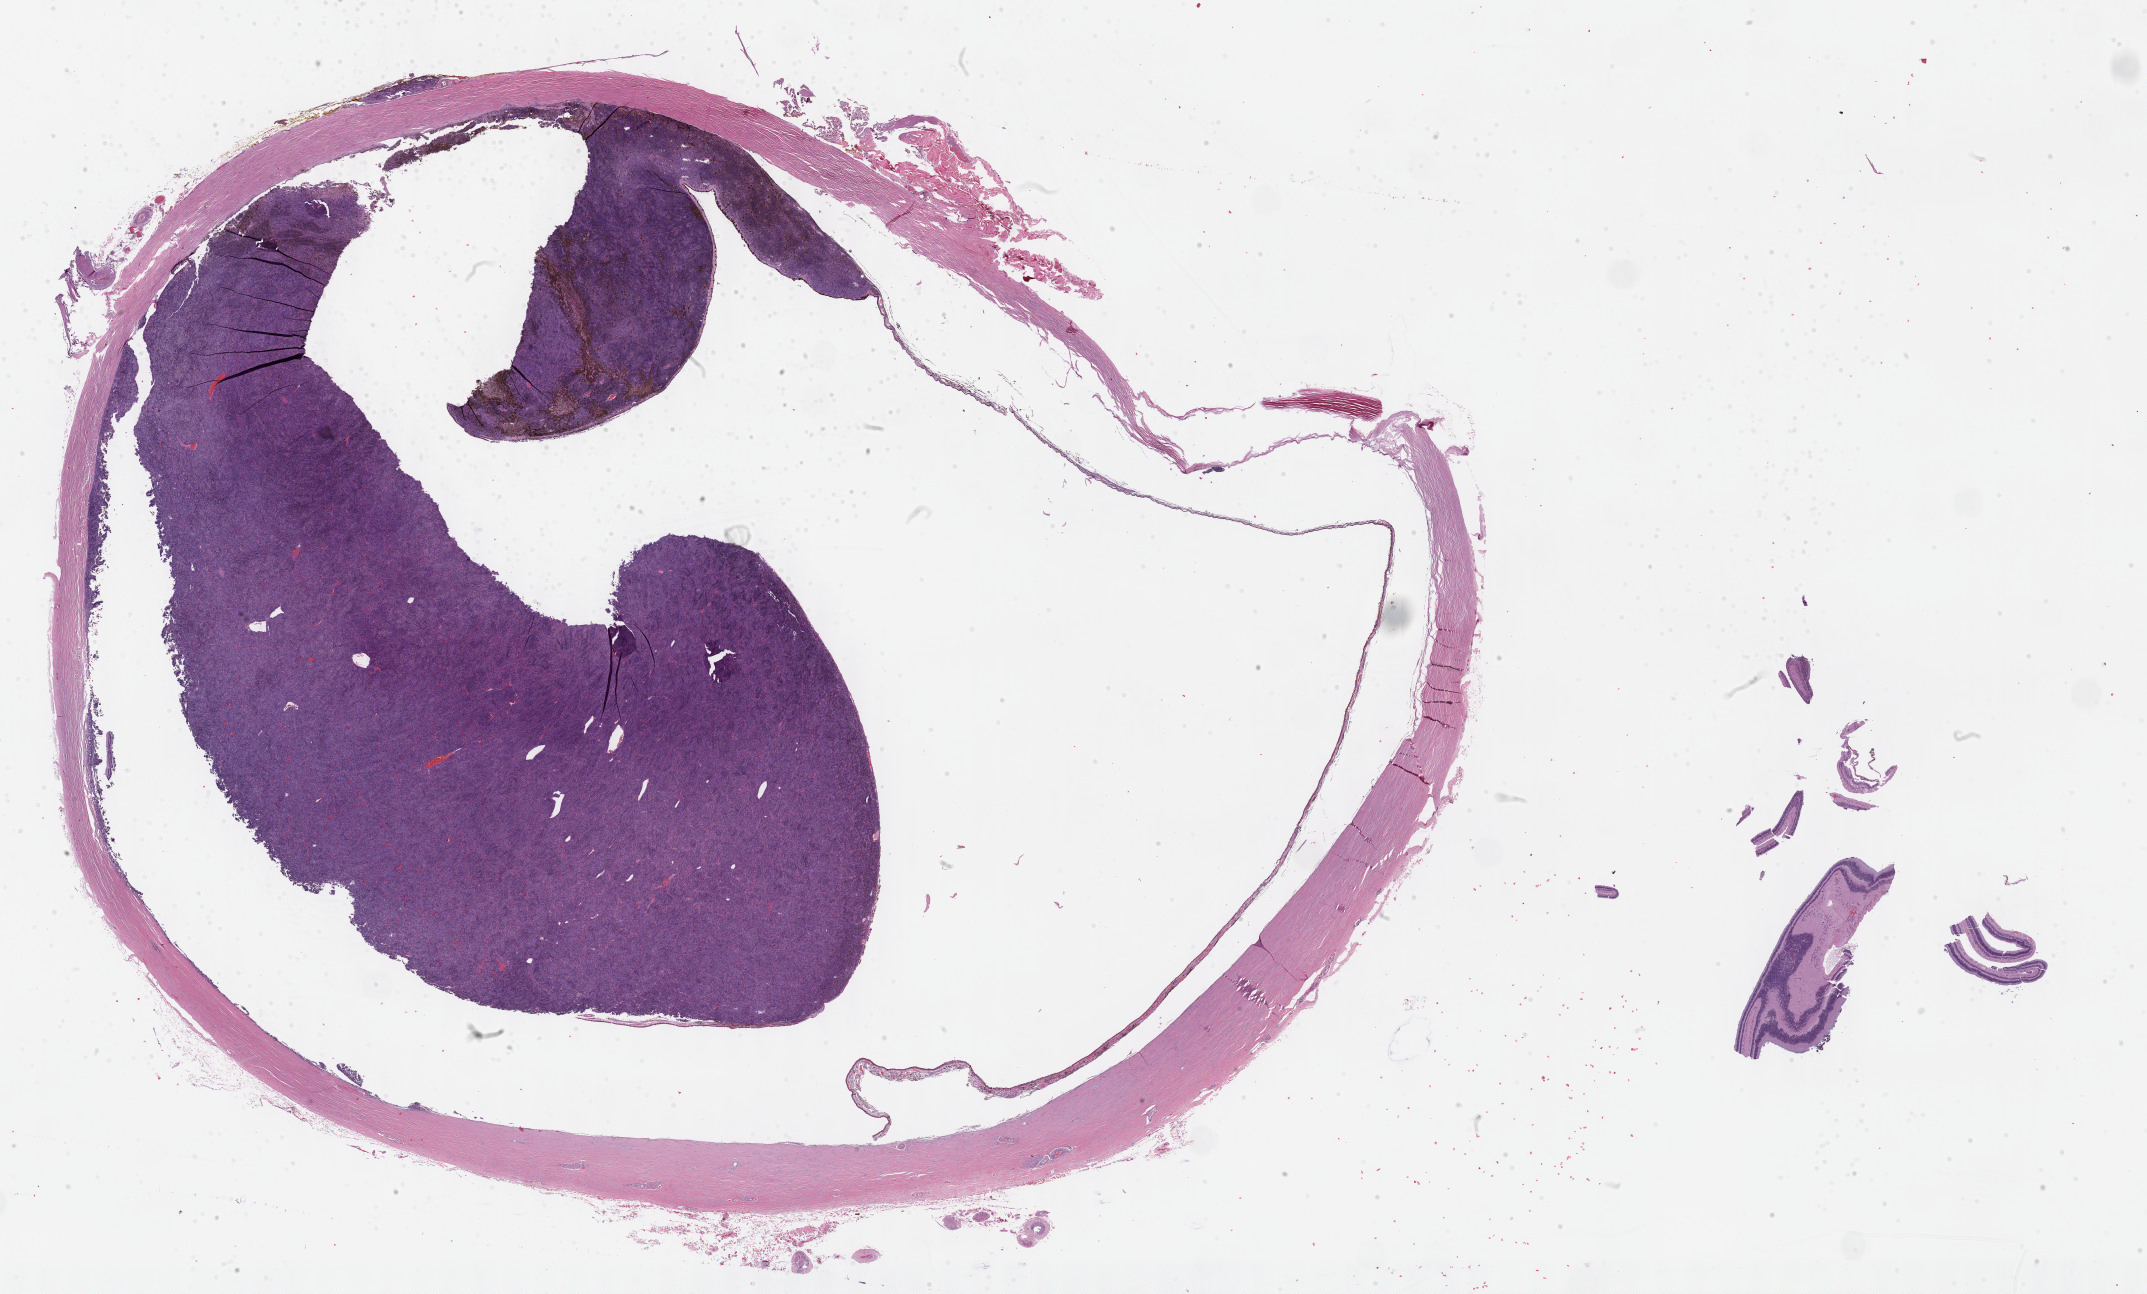
H&E-stained whole-slide image — shown as a low-resolution overview of the whole scanned area (about 34.7 x 20.9 mm, acquisition: 40x scan), formalin-fixed paraffin-embedded (FFPE) diagnostic section, sample: primary tumour, uvea. Male patient; age at initial diagnosis 75 years.
* AJCC pathologic stage: IV (7th edition)
* laterality: right
* histologic diagnosis: Mixed epithelioid and spindle cell melanoma (choroid)